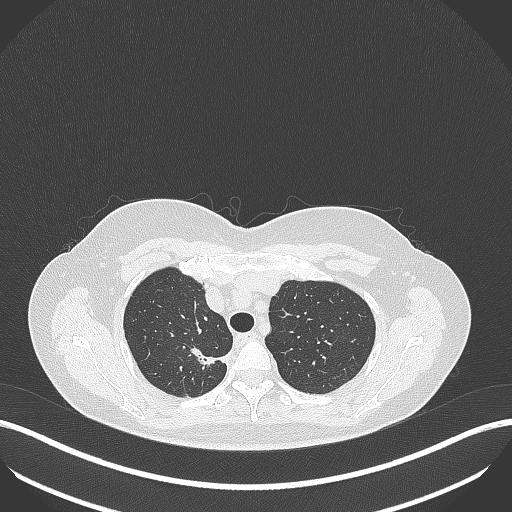
Chest CT, one axial slice. Position 316 of 386 along the scan axis. Lung window (W 1500 / L -600 HU). 512 × 512 image matrix, field of view 400 × 400 mm. Patient: female, 65 years. From the clinical record (not read from this slice): clinical TNM (as recorded): T1b N0 M0.
Structures marked on this image (bounding box drawn by a radiologist):
- lung tumour (recorded histology: adenocarcinoma): bounding box <189,343,231,370> (left, top, right, bottom; pixels)